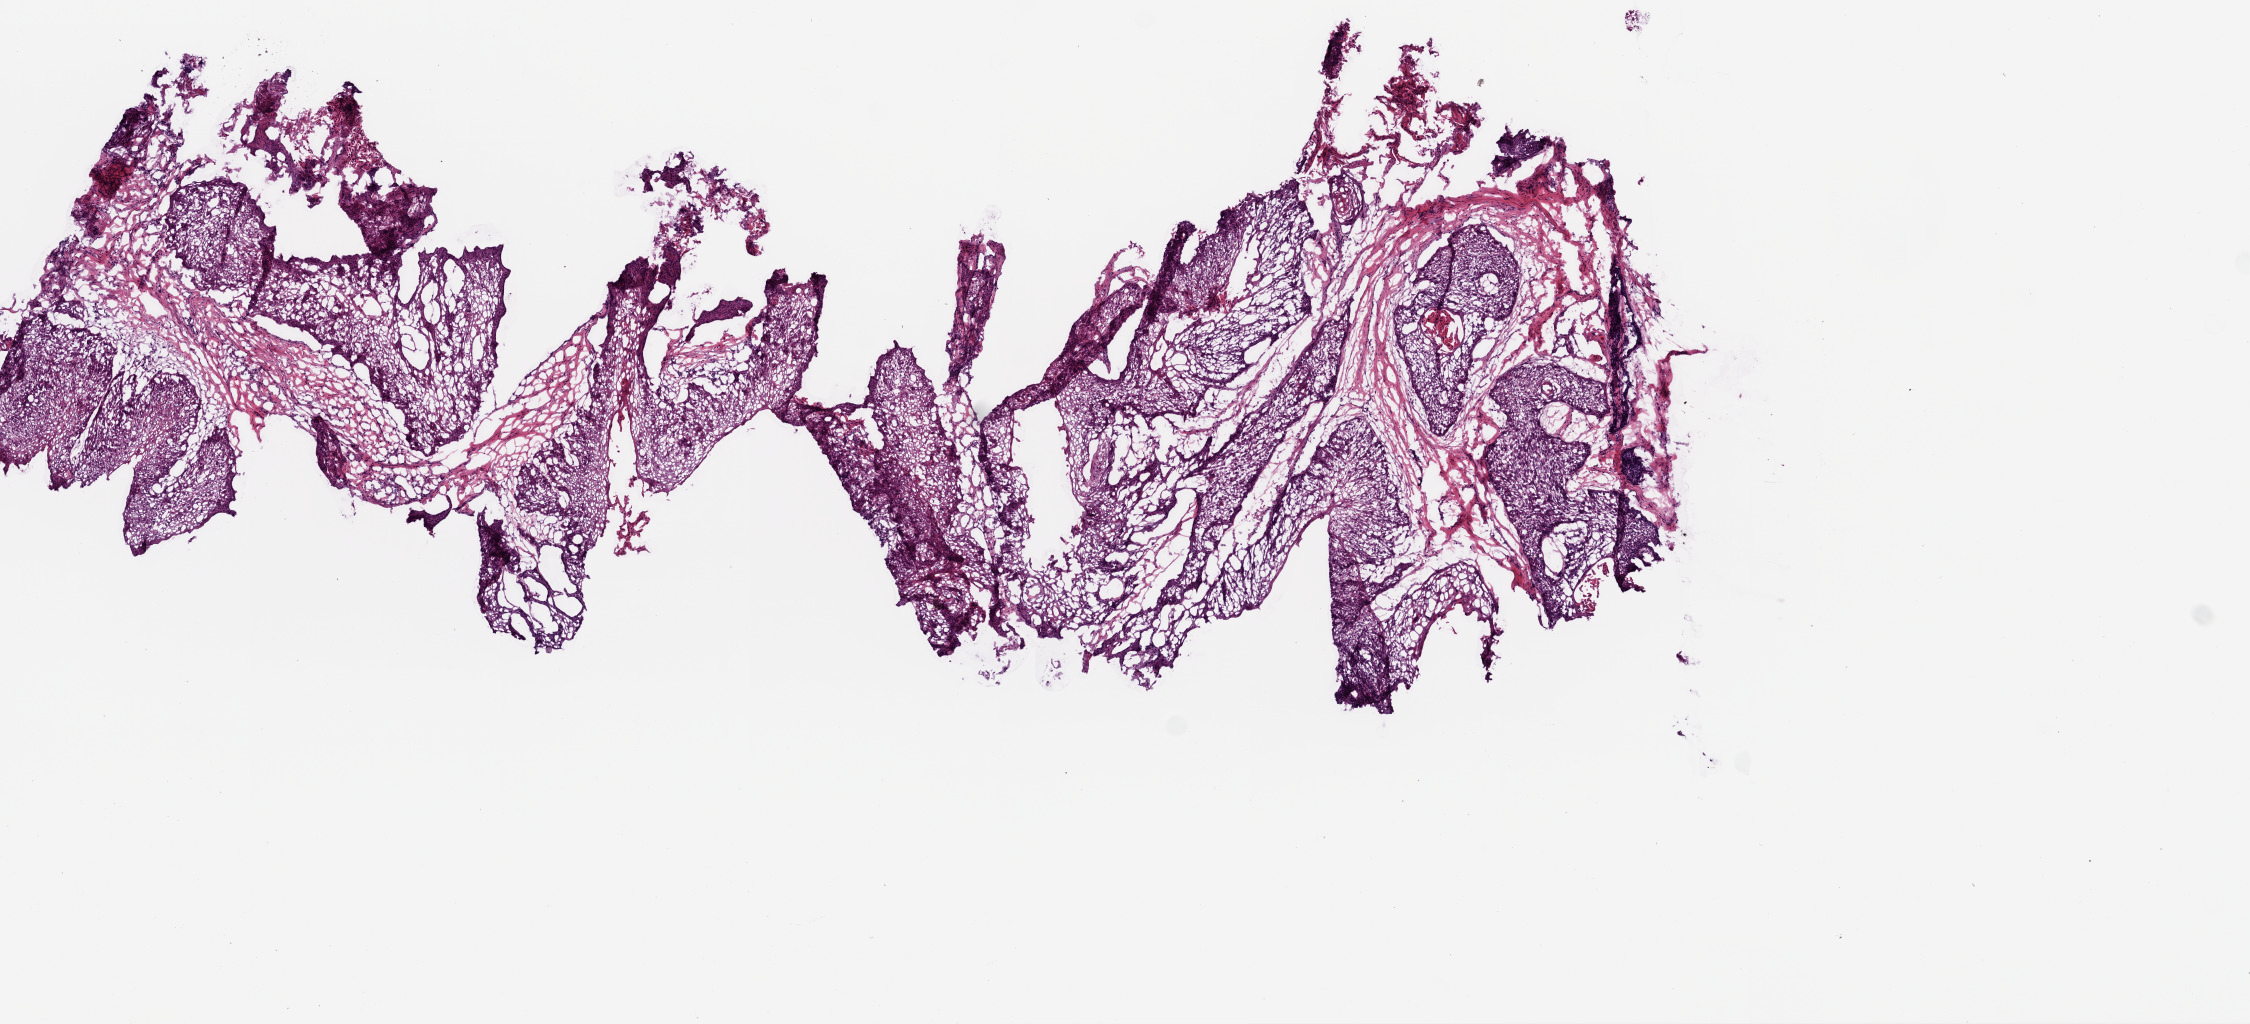
Whole-slide histology image, H&E — whole scanned area (about 9.0 x 4.1 mm, acquisition: 20x scan) shown as a low-resolution overview, frozen section from the top of the tissue portion, head and neck, primary tumour sample. Patient: male, age at initial diagnosis 75 years. Histologic grade: G2 (moderately differentiated). Composition of this section per pathologist review: tumour cells 75%, tumour nuclei 80%, normal cells 10%, stromal cells 15%, necrosis 0%.
AJCC pathologic stage: IVA (6th edition). Pathologic diagnosis: Squamous cell carcinoma, NOS (gum, NOS).